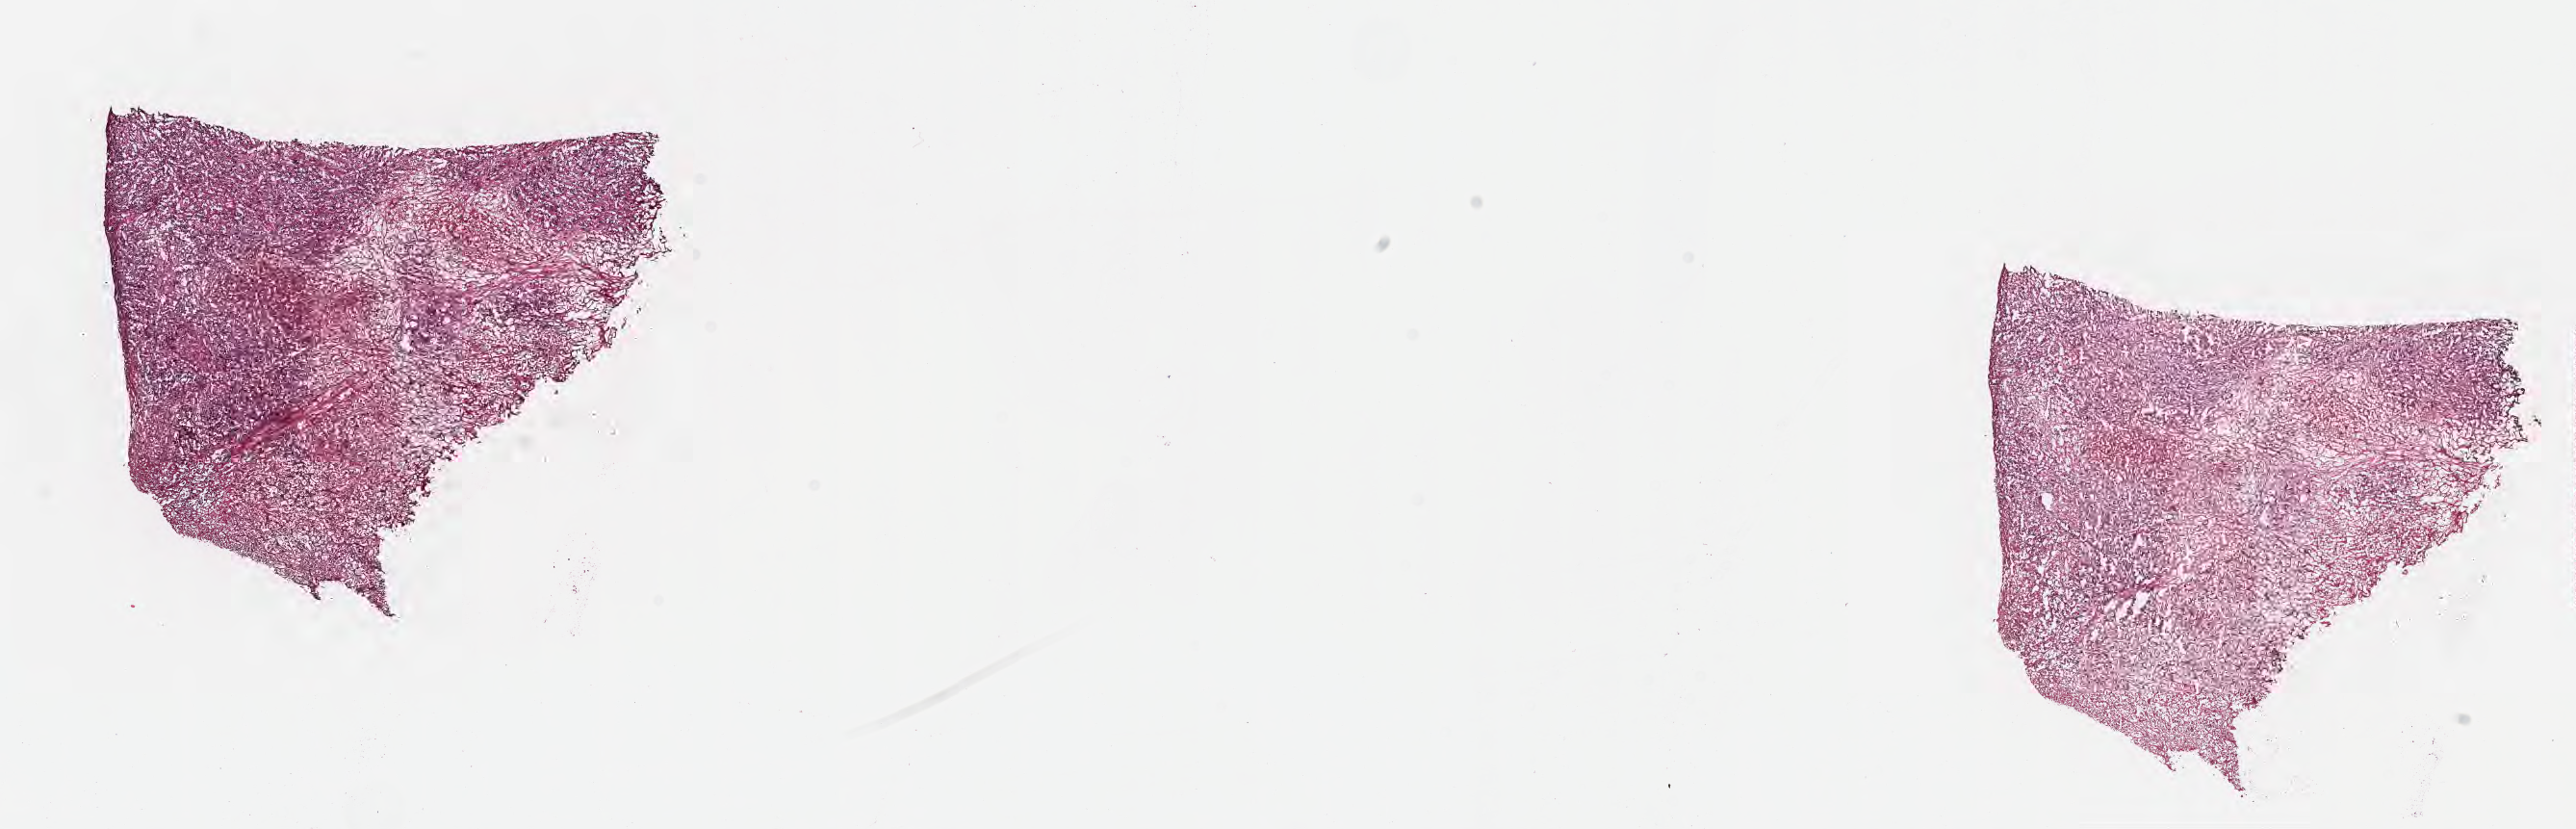
Whole-slide image, haematoxylin and eosin stain — whole scanned area (about 21.6 x 7.0 mm) shown as a low-resolution overview, cryosection, specimen: primary tumor, site: extrahepatic bile duct. Female patient; age at initial diagnosis 64 years. Composition of this section per pathologist review: tumor cells 50%, tumor nuclei 60%, stromal cells 50%, necrosis 0%, normal cells 0%. Infiltration values recorded for this section: lymphocyte infiltration 0%, monocyte infiltration 0%, neutrophil infiltration 0%.
AJCC pathologic stage: Stage IIIB. Histologic diagnosis: Cholangiocarcinoma. Section: bottom of the tissue portion.